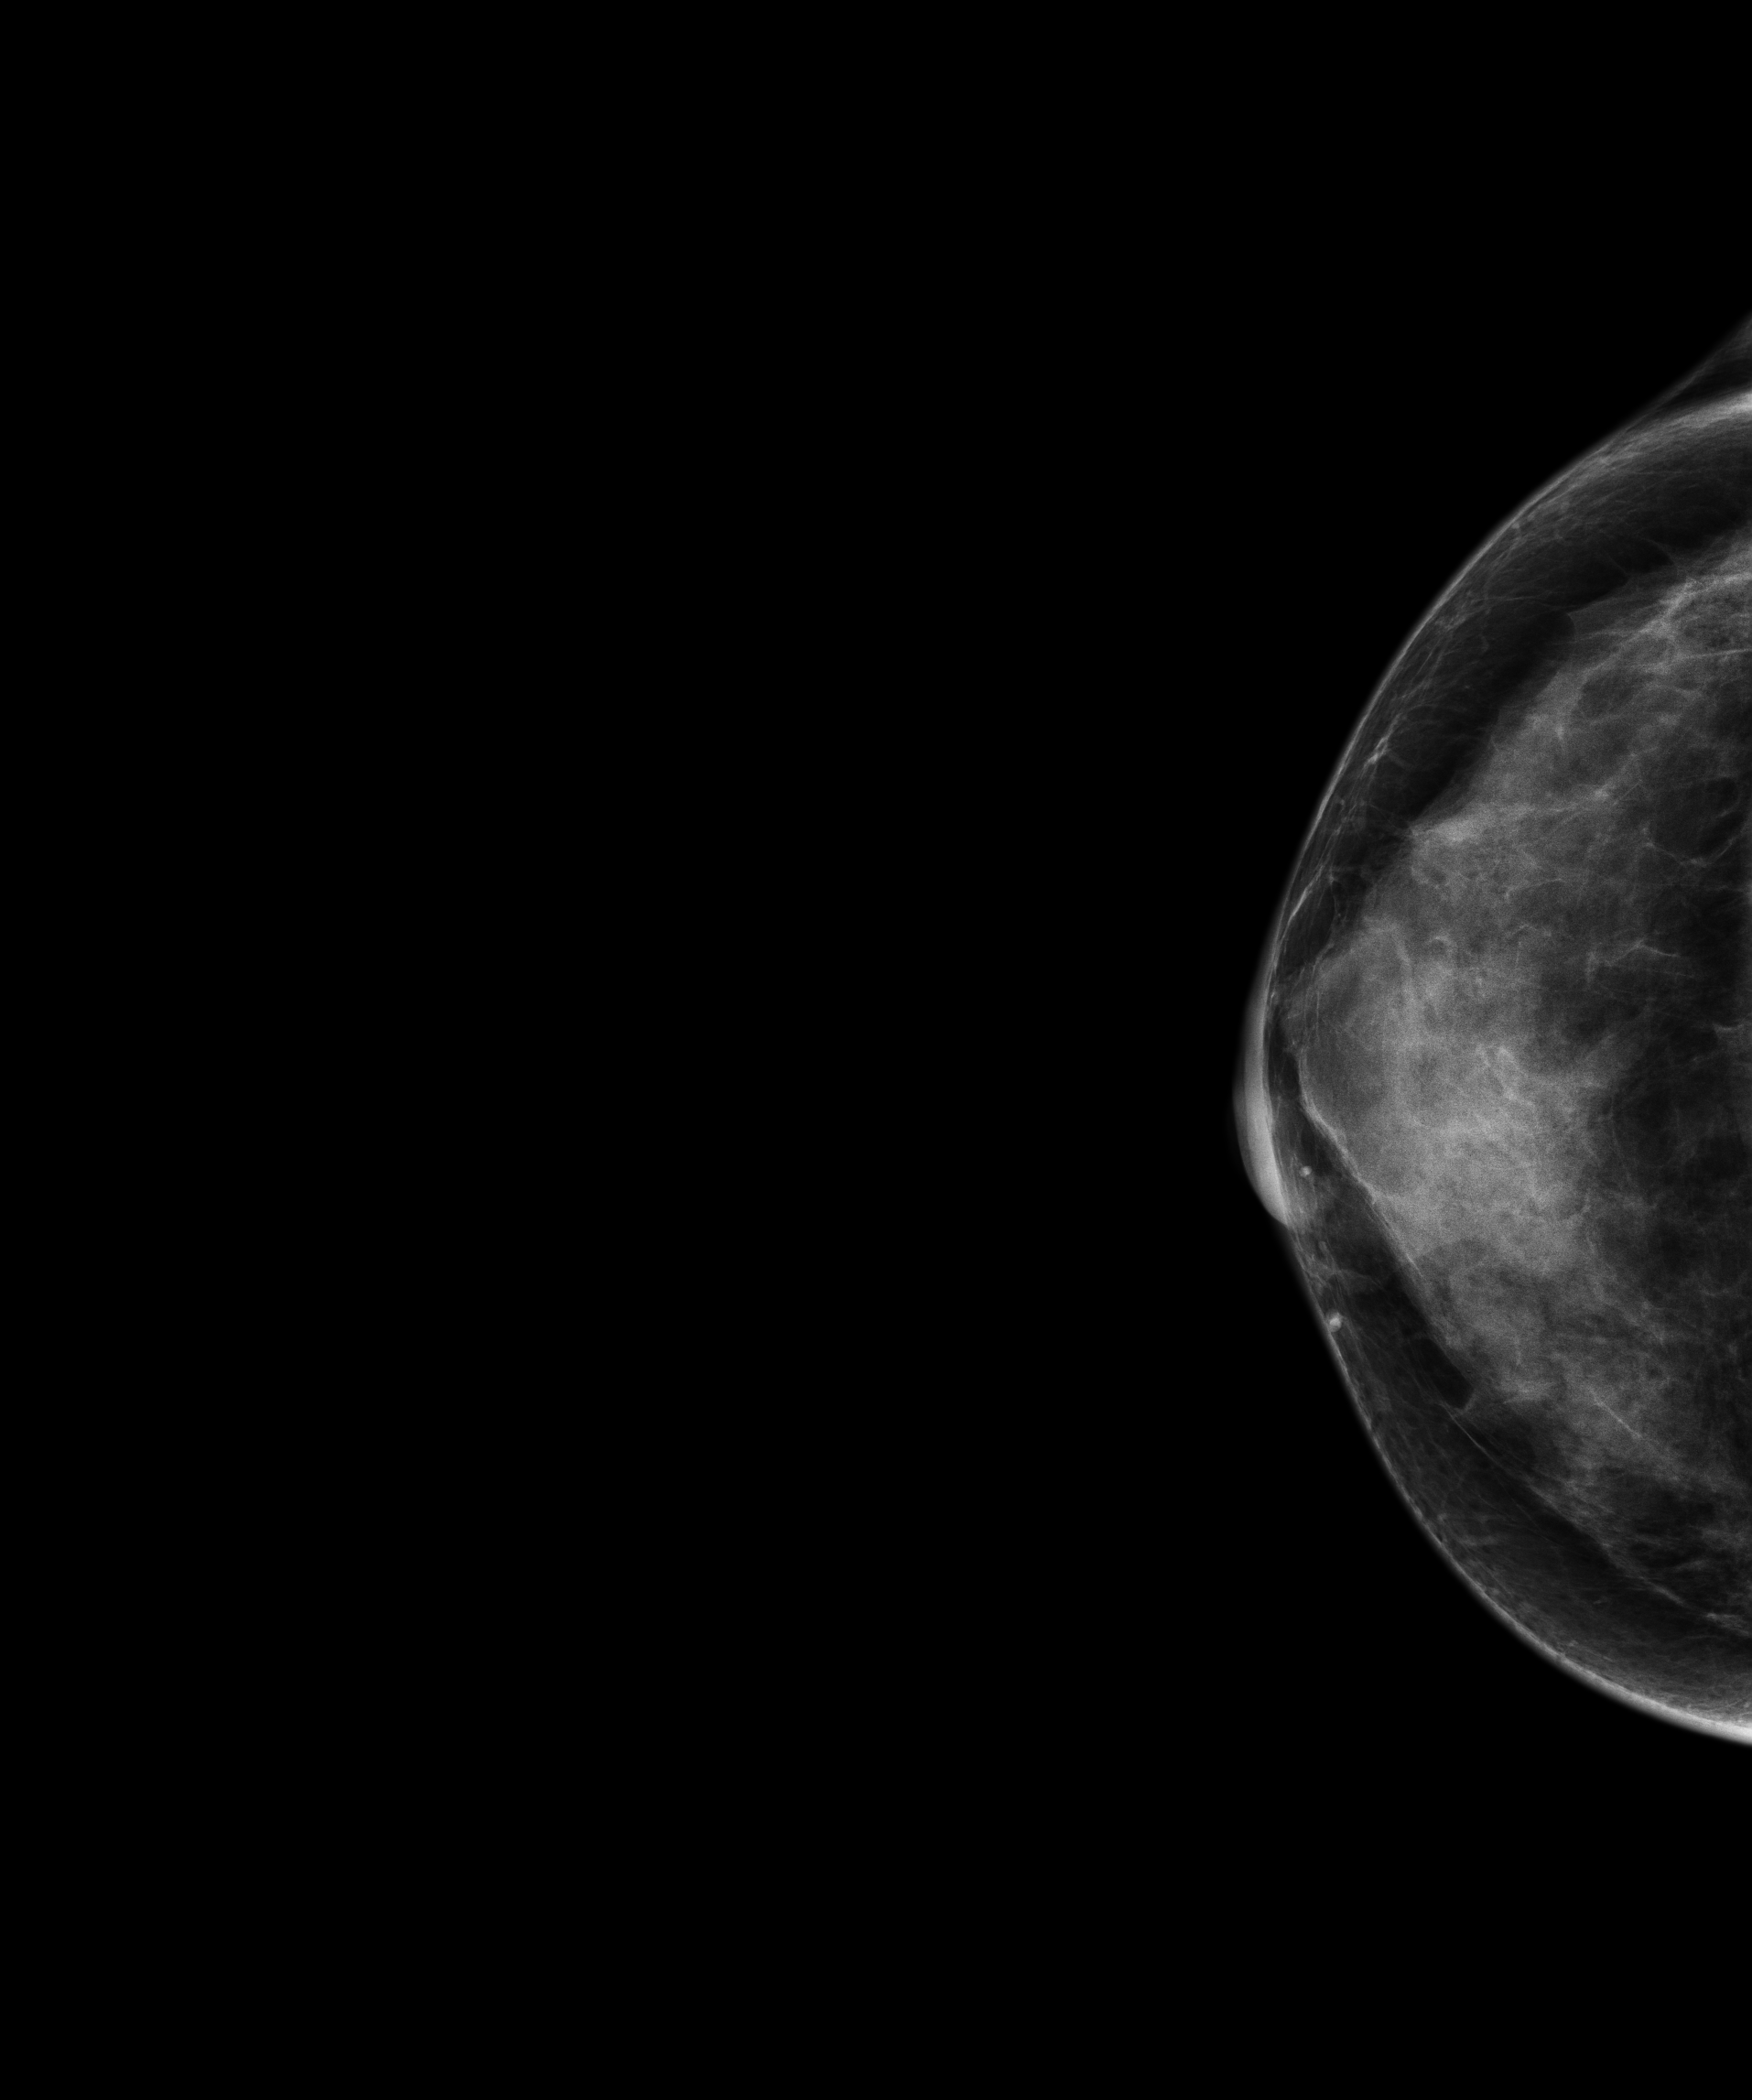
Digital mammogram (FFDM), right breast, craniocaudal (CC) view, screening examination, compressed breast thickness 39 mm, system: Senographe Essential ADS_56.21.3. Female patient, age 46 years.
BI-RADS breast density category at the screening exam (both breasts, scale 1–4): 4. Final BI-RADS category for the screening round (tomosynthesis exam, both breasts): category 1. Recall: no recall after this screen.